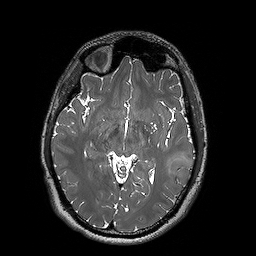
Brain MRI from a brain-tumour surgery series, one axial slice. Position 95 of 192 along the scan axis. 256 × 256 image matrix. From the clinical record (not read from this slice): histopathology: Oligodendroglioma; WHO grade: 2; IDH mutation: yes.
Annotated regions visible in this slice (manually delineated by an expert):
- tumour: box from (x=159, y=155) to (x=193, y=182) px